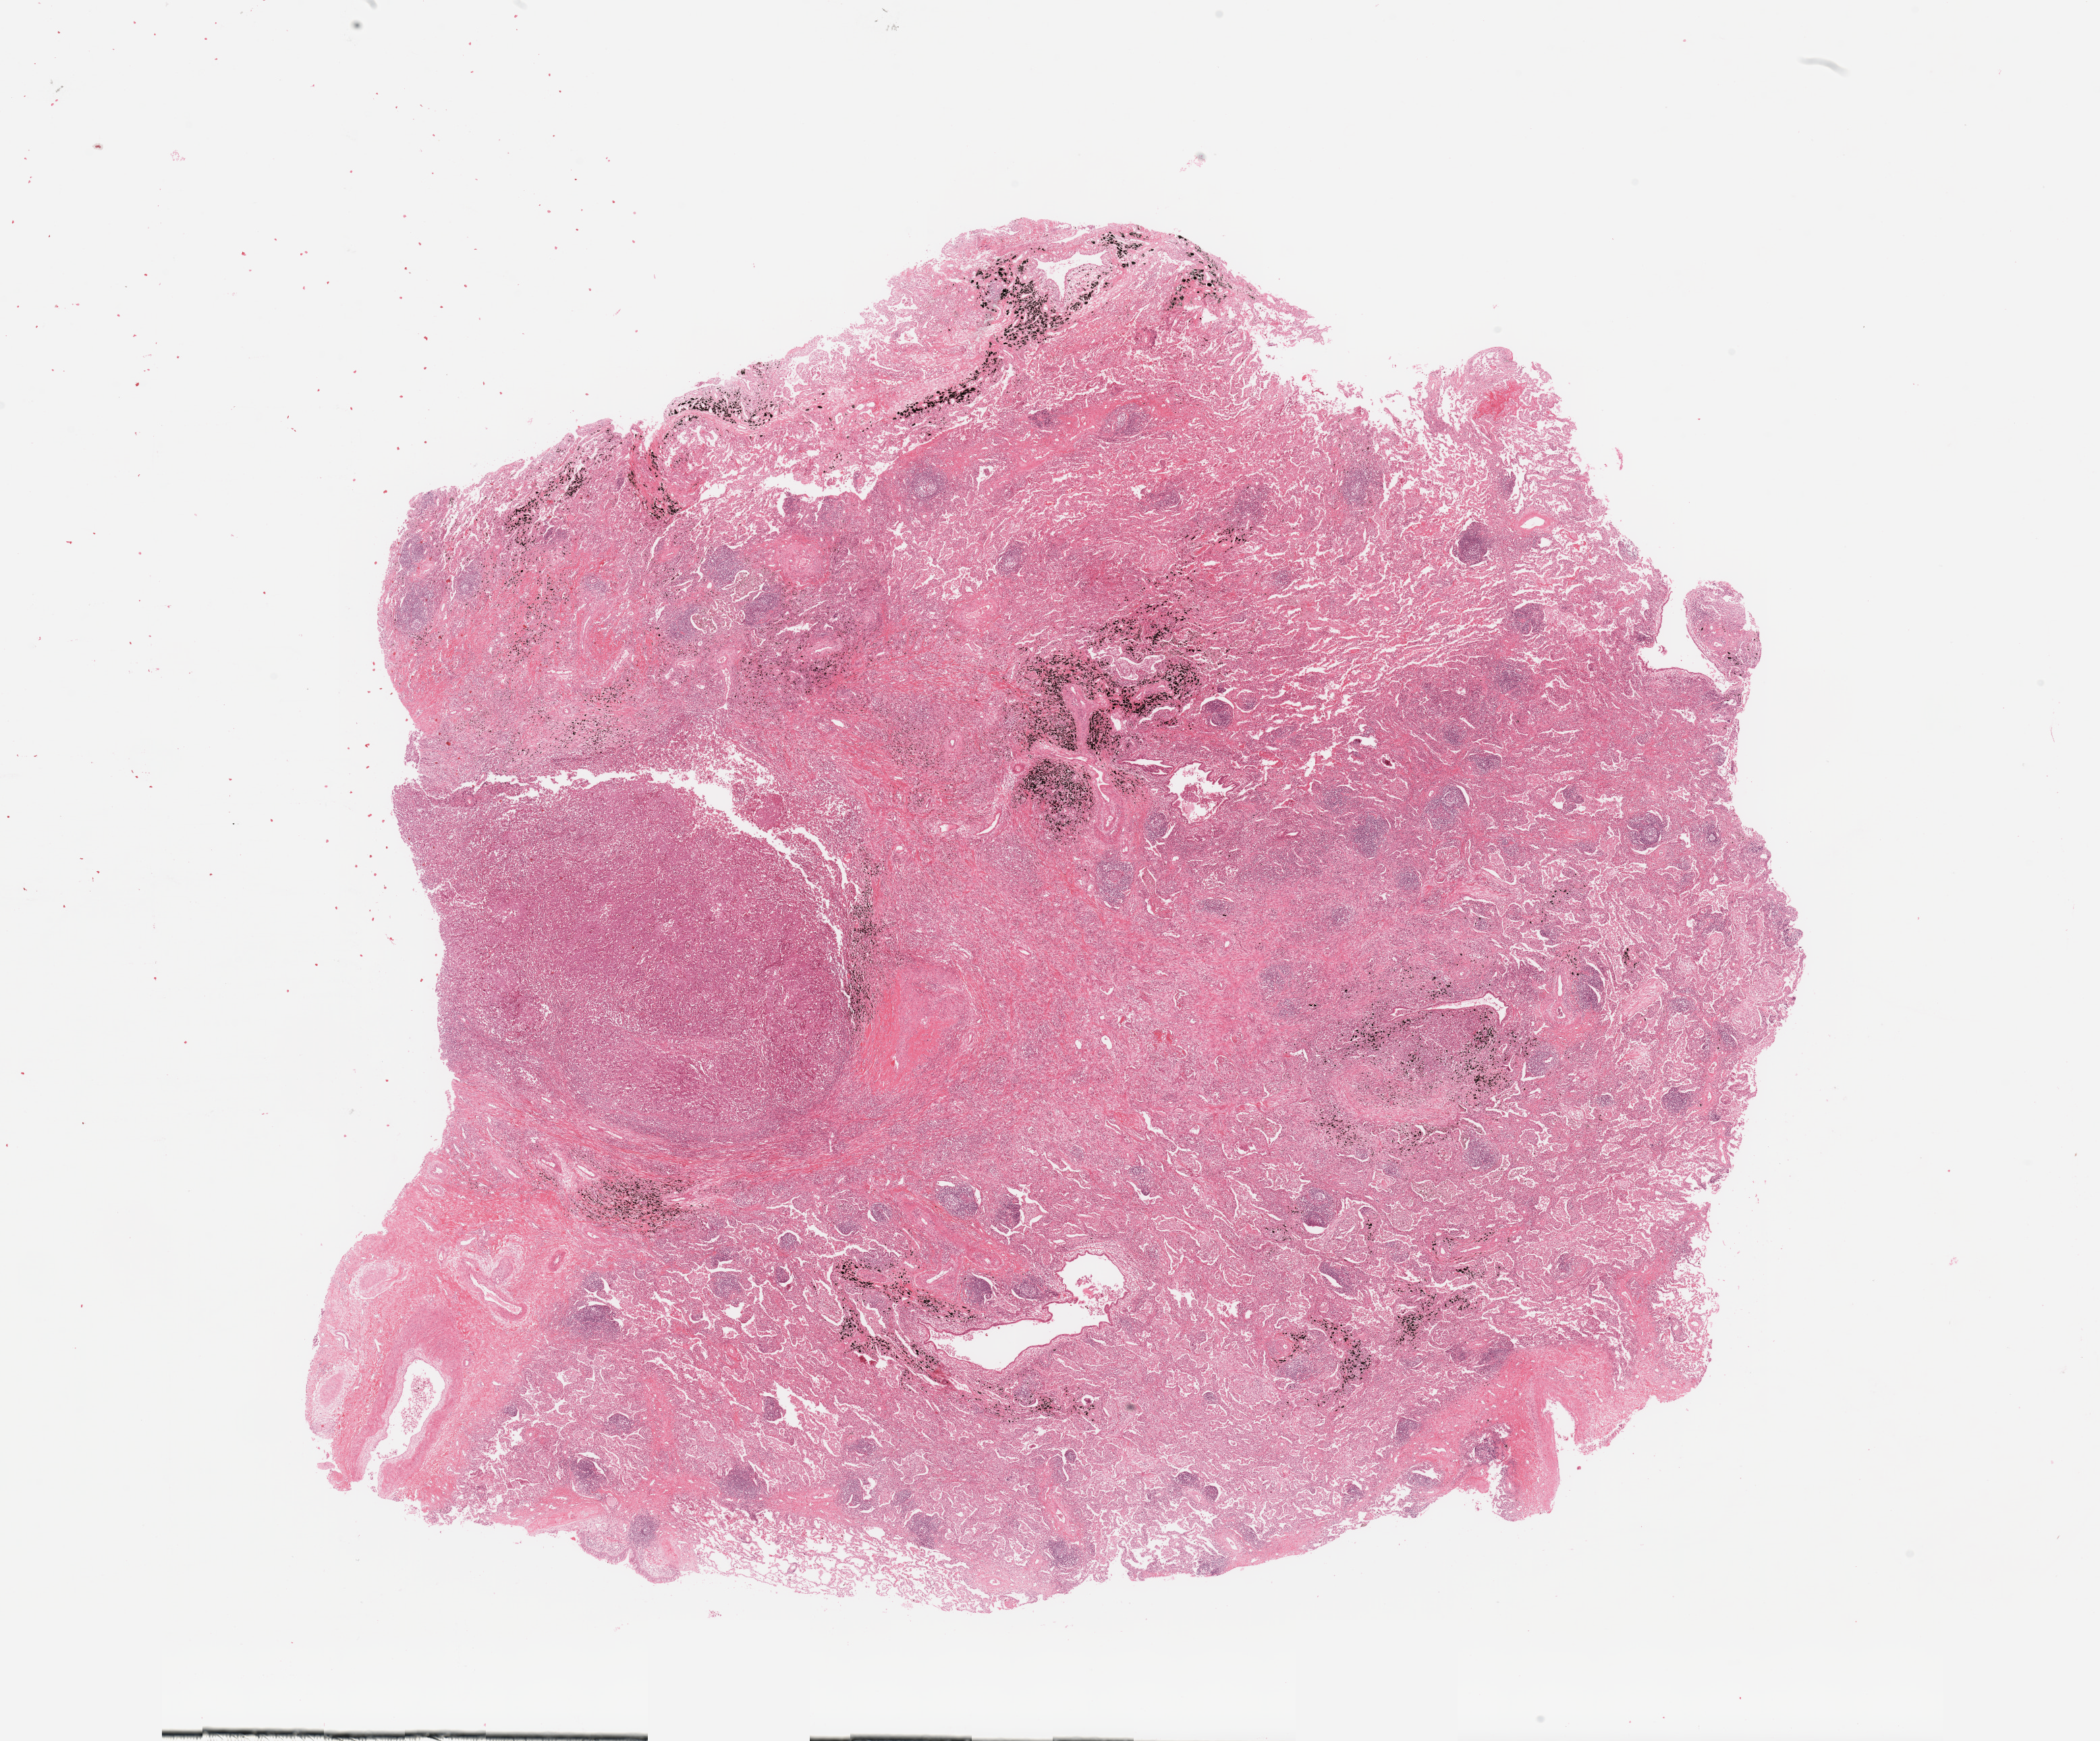
H&E-stained whole-slide image, low-resolution overview of the scanned area, about 24.6 x 20.4 mm; tumour tissue sample, lung. Male, 54 y/o. Histologic grade: G3 (poorly differentiated).
Diagnosis: Adenocarcinoma, NOS. AJCC pathologic stage: IIIA.